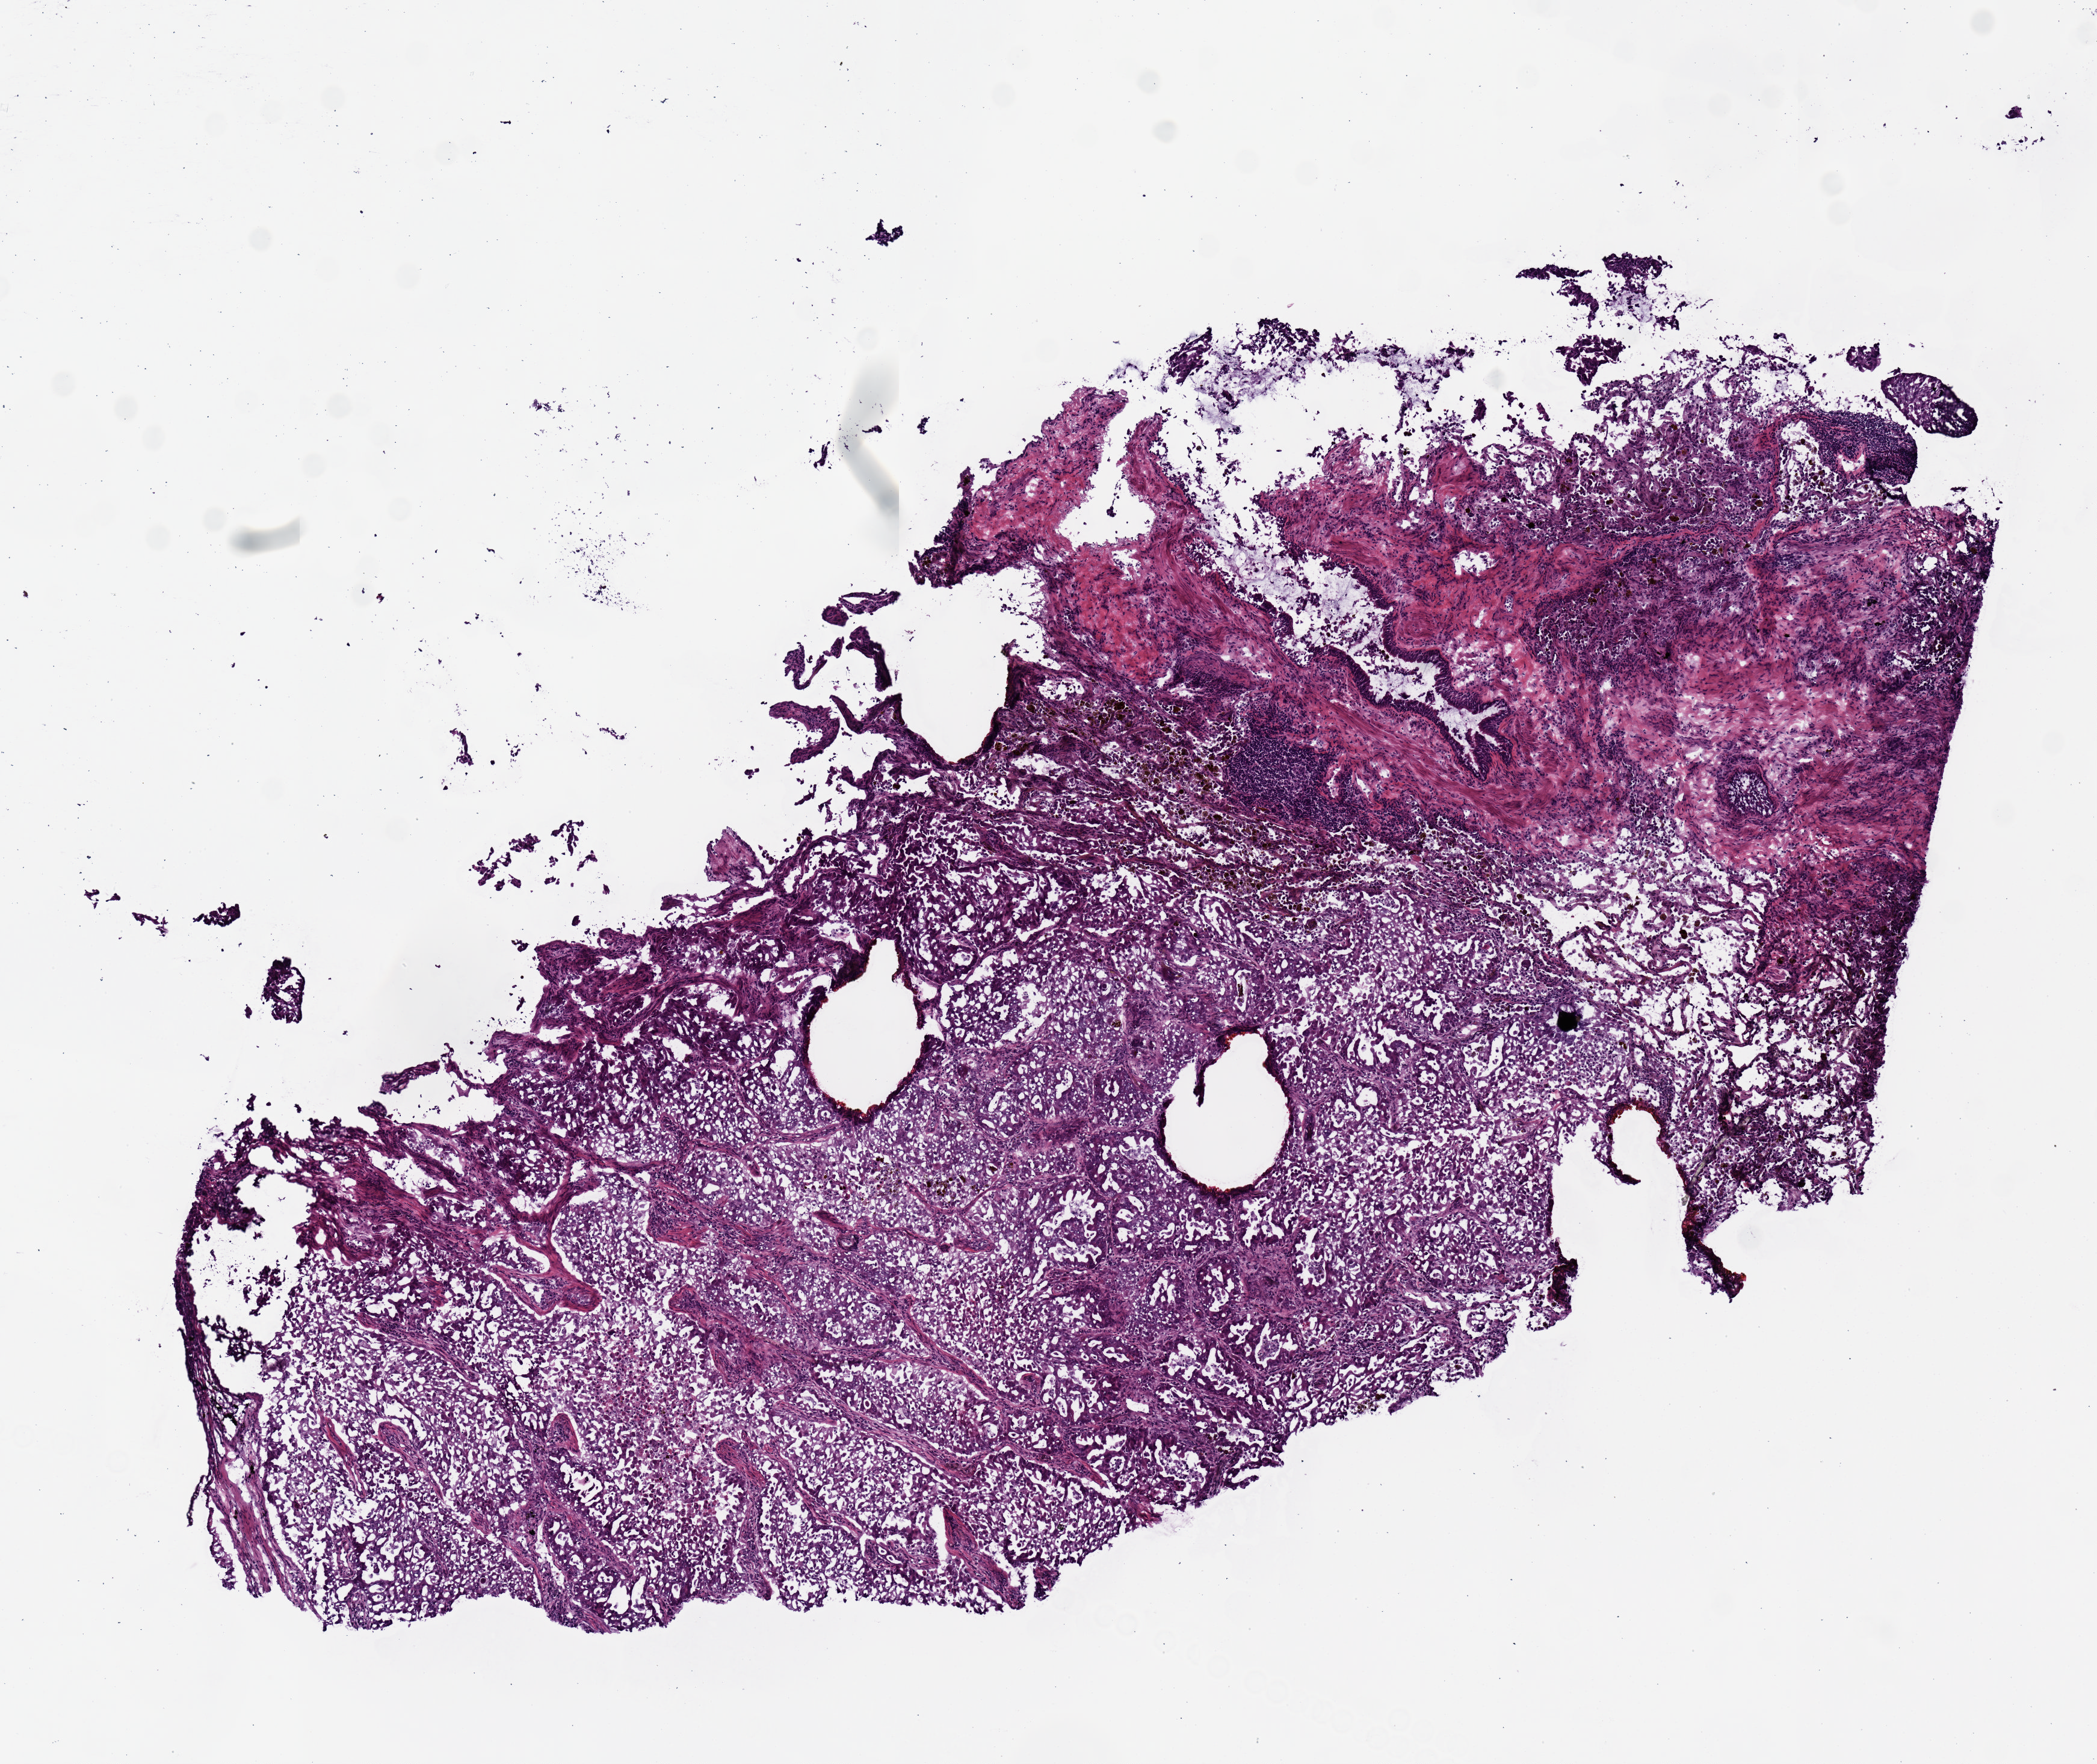
H&E-stained whole-slide image, whole scanned area (about 6.9 x 5.8 mm) shown as a low-resolution overview. Frozen section from the top of the tissue portion. Lung, primary tumour sample. Female, age 54 years at initial diagnosis. Pathologist review of this section (percent, as recorded): tumour cells 90%, tumour nuclei 80%, normal cells 0%, stromal cells 10%, necrosis 0%. Inflammatory infiltration, as recorded: lymphocyte infiltration 9%, monocyte infiltration 2%, neutrophil infiltration 0%.
• AJCC pathologic stage: IIIA (7th edition)
• laterality: left
• pathologic diagnosis: Adenocarcinoma with mixed subtypes (upper lobe, lung)